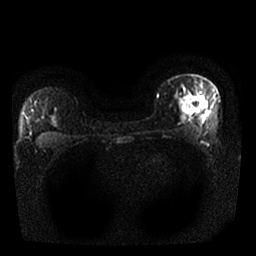
Breast MRI, one axial slice. Position 20 of 25 along the scan axis. Diffusion-weighted series; image 2 of 4 stored at this slice position (different b-values; order by instance number). 1.5 T. 4 mm slice thickness. 256 × 256 image matrix, field of view 320 × 320 mm. Female patient.
Annotated regions visible in this slice (manually delineated by an expert):
- tumour on diffusion-weighted imaging: bounding box [x1, y1, x2, y2] px = [182, 99, 201, 112]